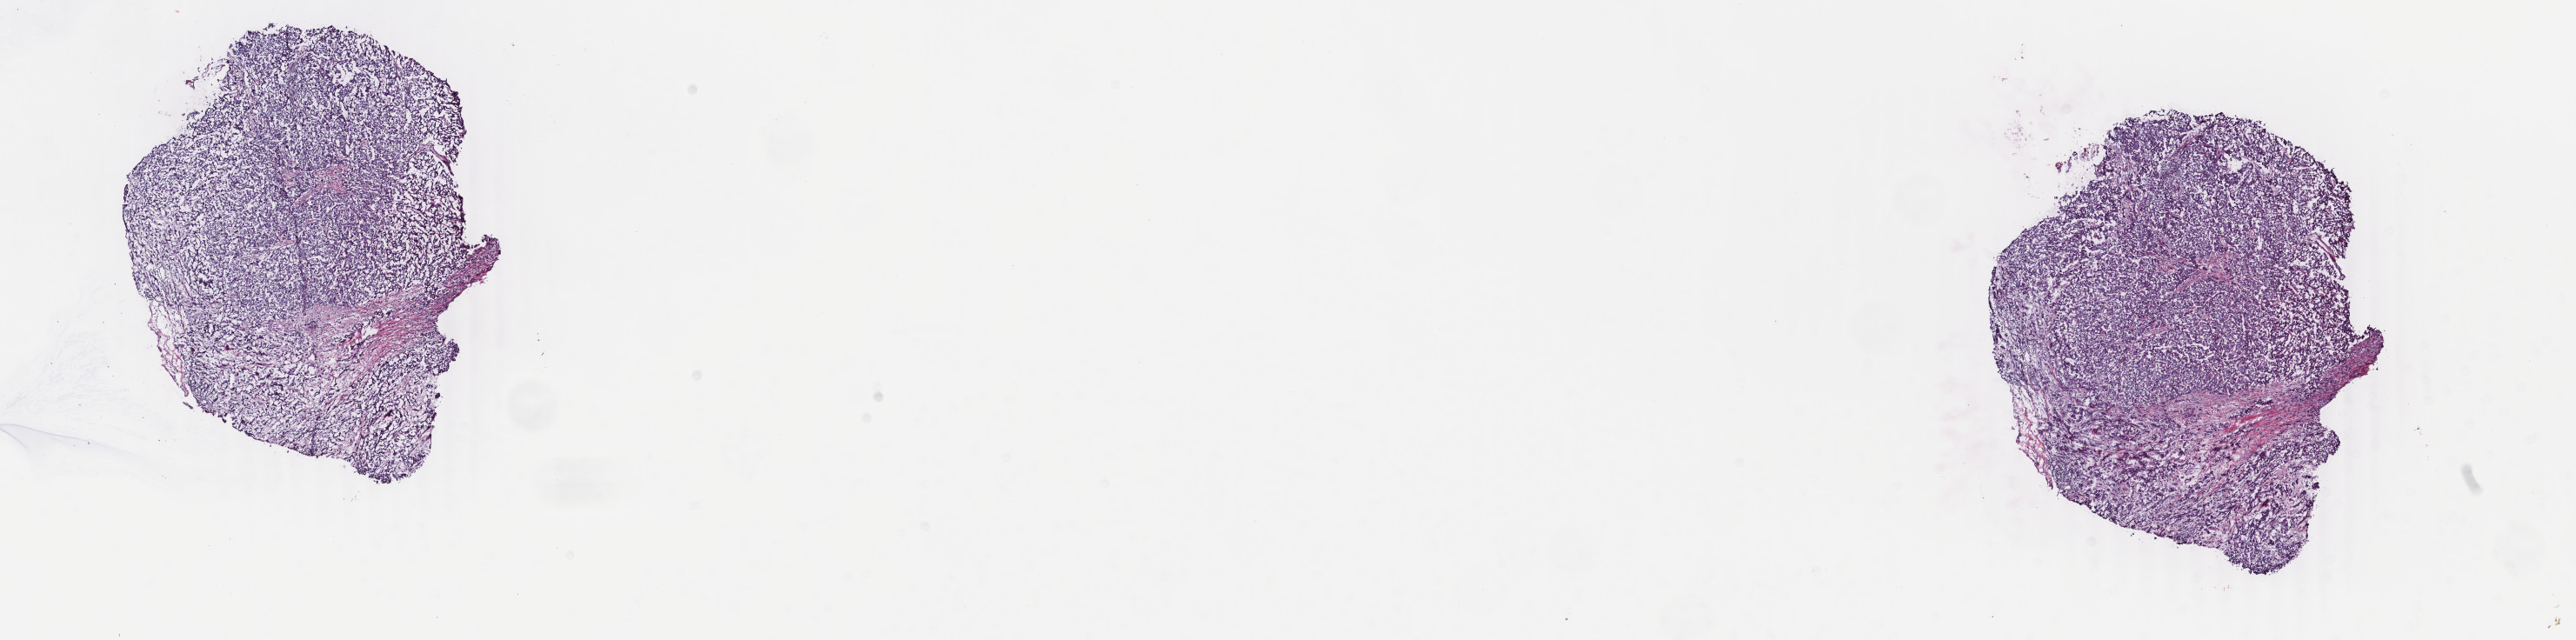
Whole-slide histology image, H&E-stained, a low-resolution overview of the entire scanned area, about 23.6 x 5.9 mm (from a 40x scan). Frozen section from the bottom of the tissue portion. Sample: primary tumour, breast. Female patient; age at initial diagnosis 29 years. Slide review estimates, as recorded: tumour cells 90%, tumour nuclei 90%, normal cells 0%, stromal cells 10%, necrosis 0%. Infiltration values recorded for this section: lymphocyte infiltration 2%, monocyte infiltration 0%, neutrophil infiltration 0%.
TNM: T1c N0 (i-) M0. Pathologic diagnosis: Infiltrating duct carcinoma, NOS. Lymph nodes positive (case pathology): 0 of 2 examined. AJCC pathologic stage: I (6th edition).